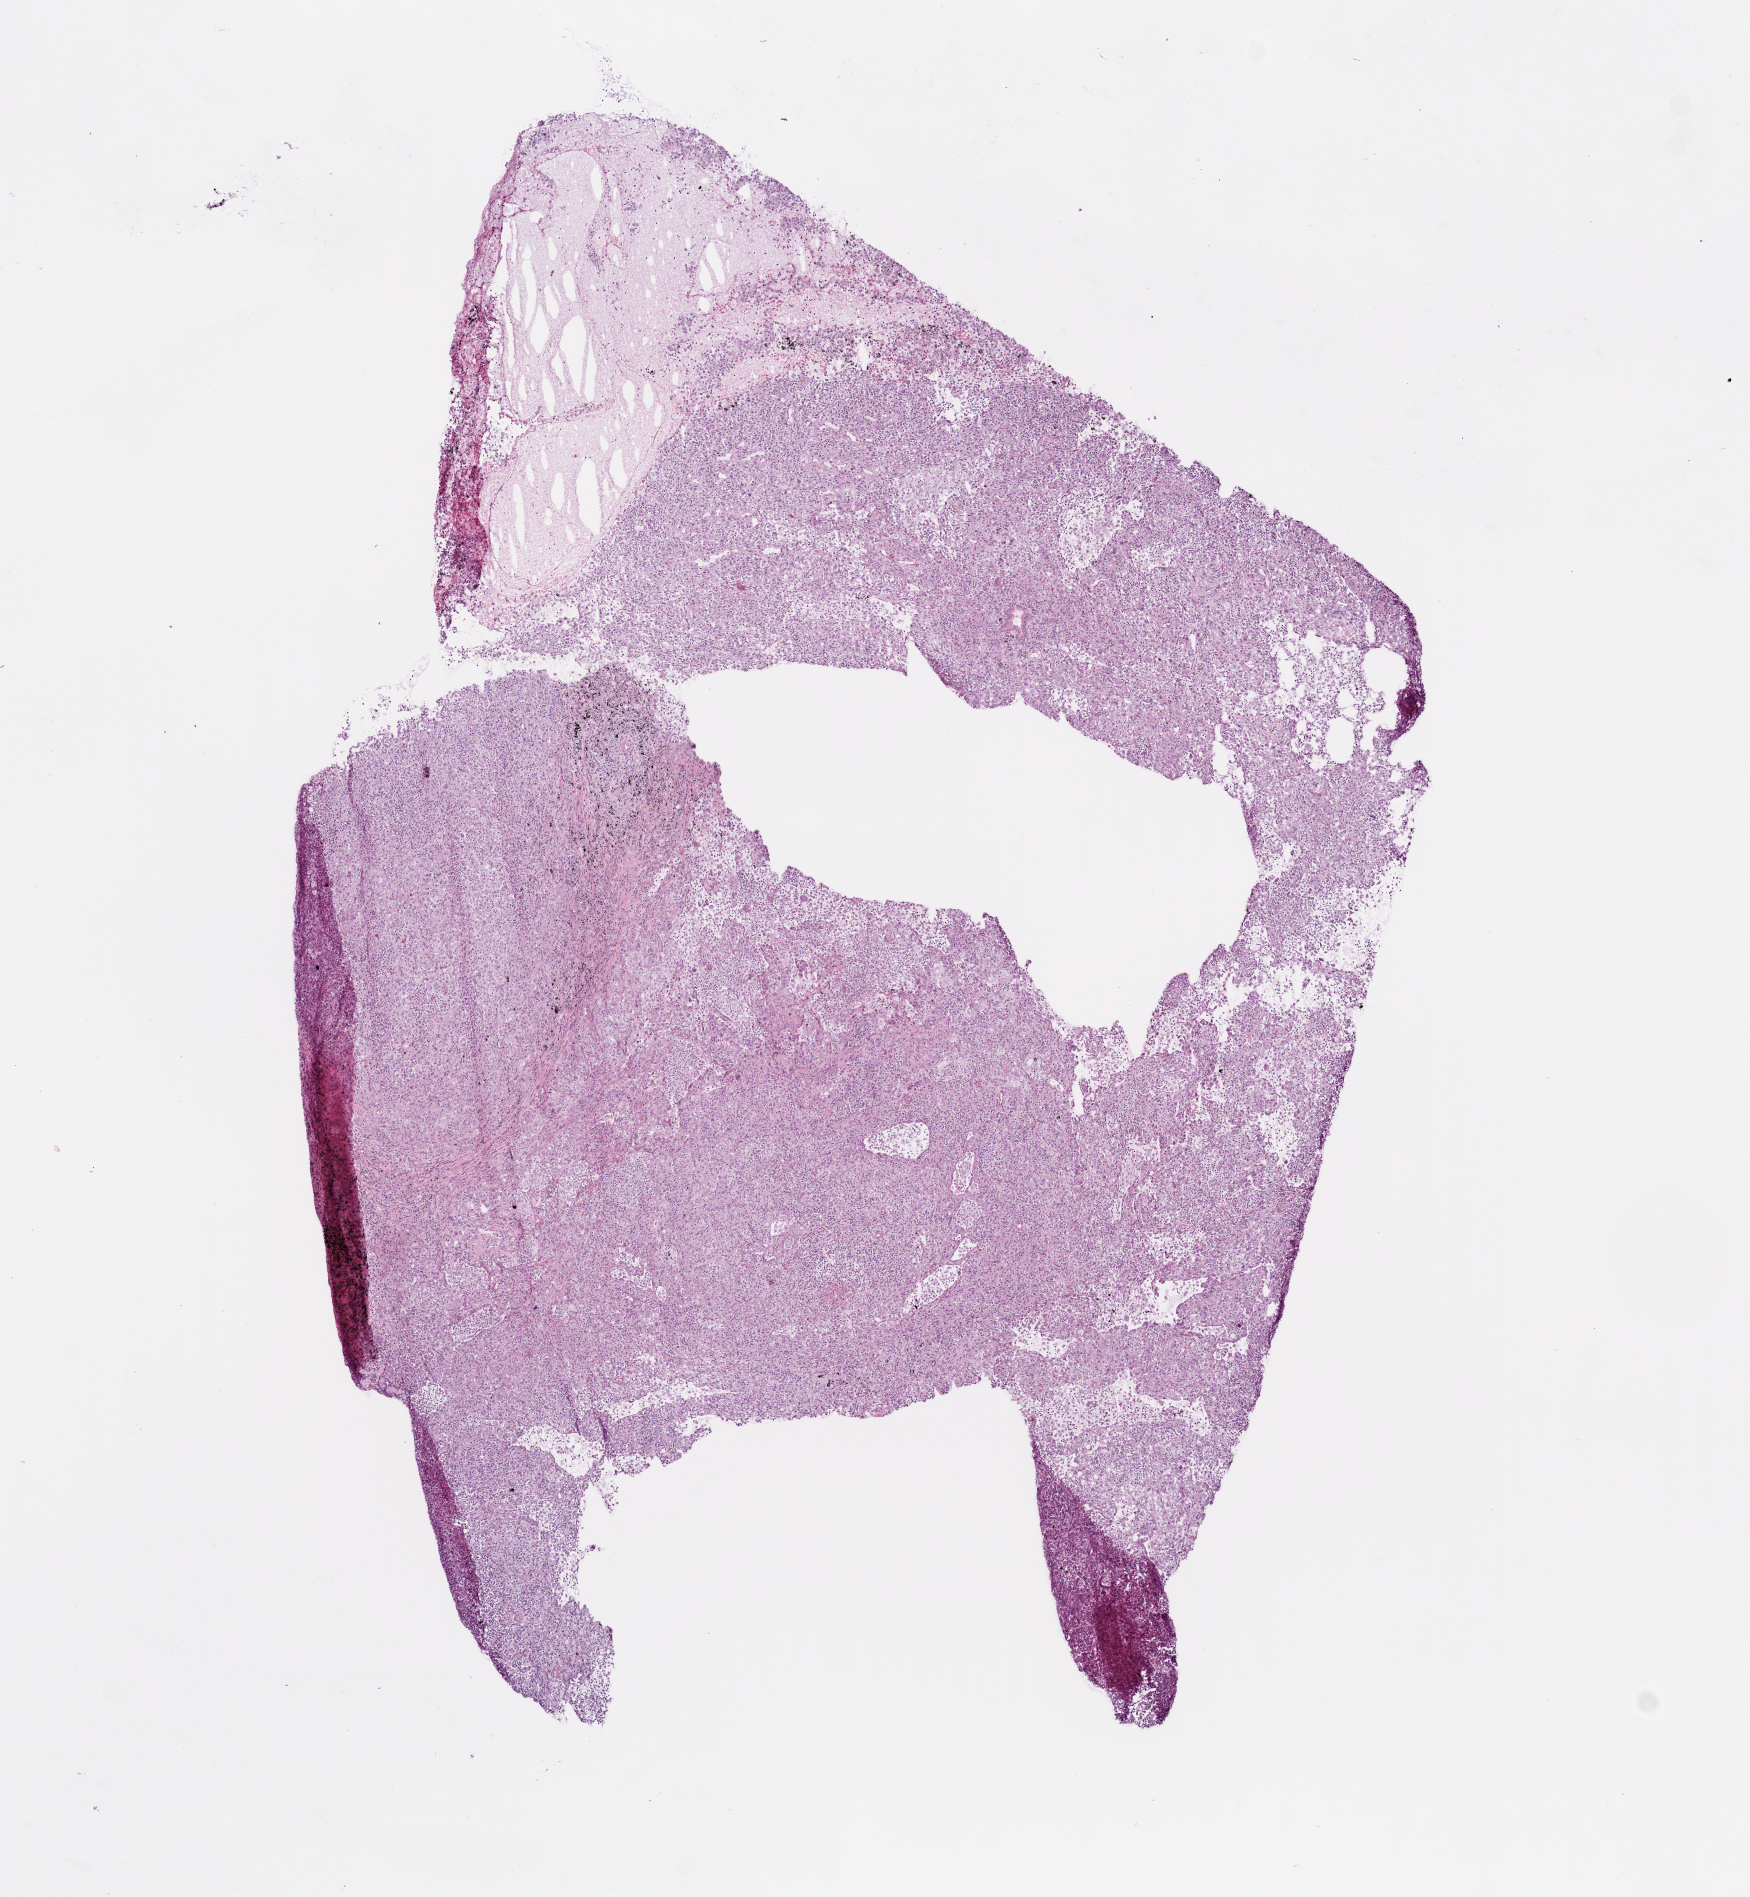
Whole-slide histology image, H&E-stained — a low-resolution overview of the entire scanned area, about 7.0 x 7.6 mm (acquisition: 20x scan). Frozen section from the top of the tissue portion. Primary tumour sample from the lung. Patient sex: male. Composition of this section per pathologist review: tumour cells 95%, tumour nuclei 70%, normal cells 0%, stromal cells 5%, necrosis 0%.
* AJCC pathologic stage: IB
* histologic diagnosis: Adenocarcinoma, NOS (upper lobe, lung)